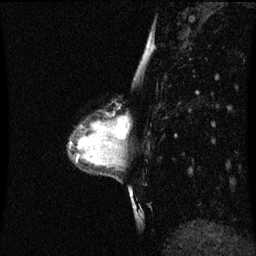
Breast MRI (dynamic contrast-enhanced), one sagittal slice. Slice 28 of 60 in the series (ordered by position). Dynamic contrast-enhanced series, image 2 of 3 at this slice position (ordered by acquisition). 1.5 T. TE 4.2 ms, TR 8.9 ms. 2 mm slice thickness. 256 × 256 image matrix, field of view 200 × 200 mm. Patient: female, 33 years. Case-level facts recorded for this patient, not image findings: setting: breast cancer imaged before/during neoadjuvant chemotherapy; receptor status: HER2-positive.
Outlined on this slice (semi-automatic segmentation, software-assisted and operator-edited):
- analysis volume of interest (the breast-tissue region the enhancement analysis was run in; not a lesion): box from (x=107, y=112) to (x=124, y=147) px
- tumour enhancement mask (voxels above the 70 % enhancement threshold inside the analysis volume of interest): (x=117, y=118)–(x=123, y=141)